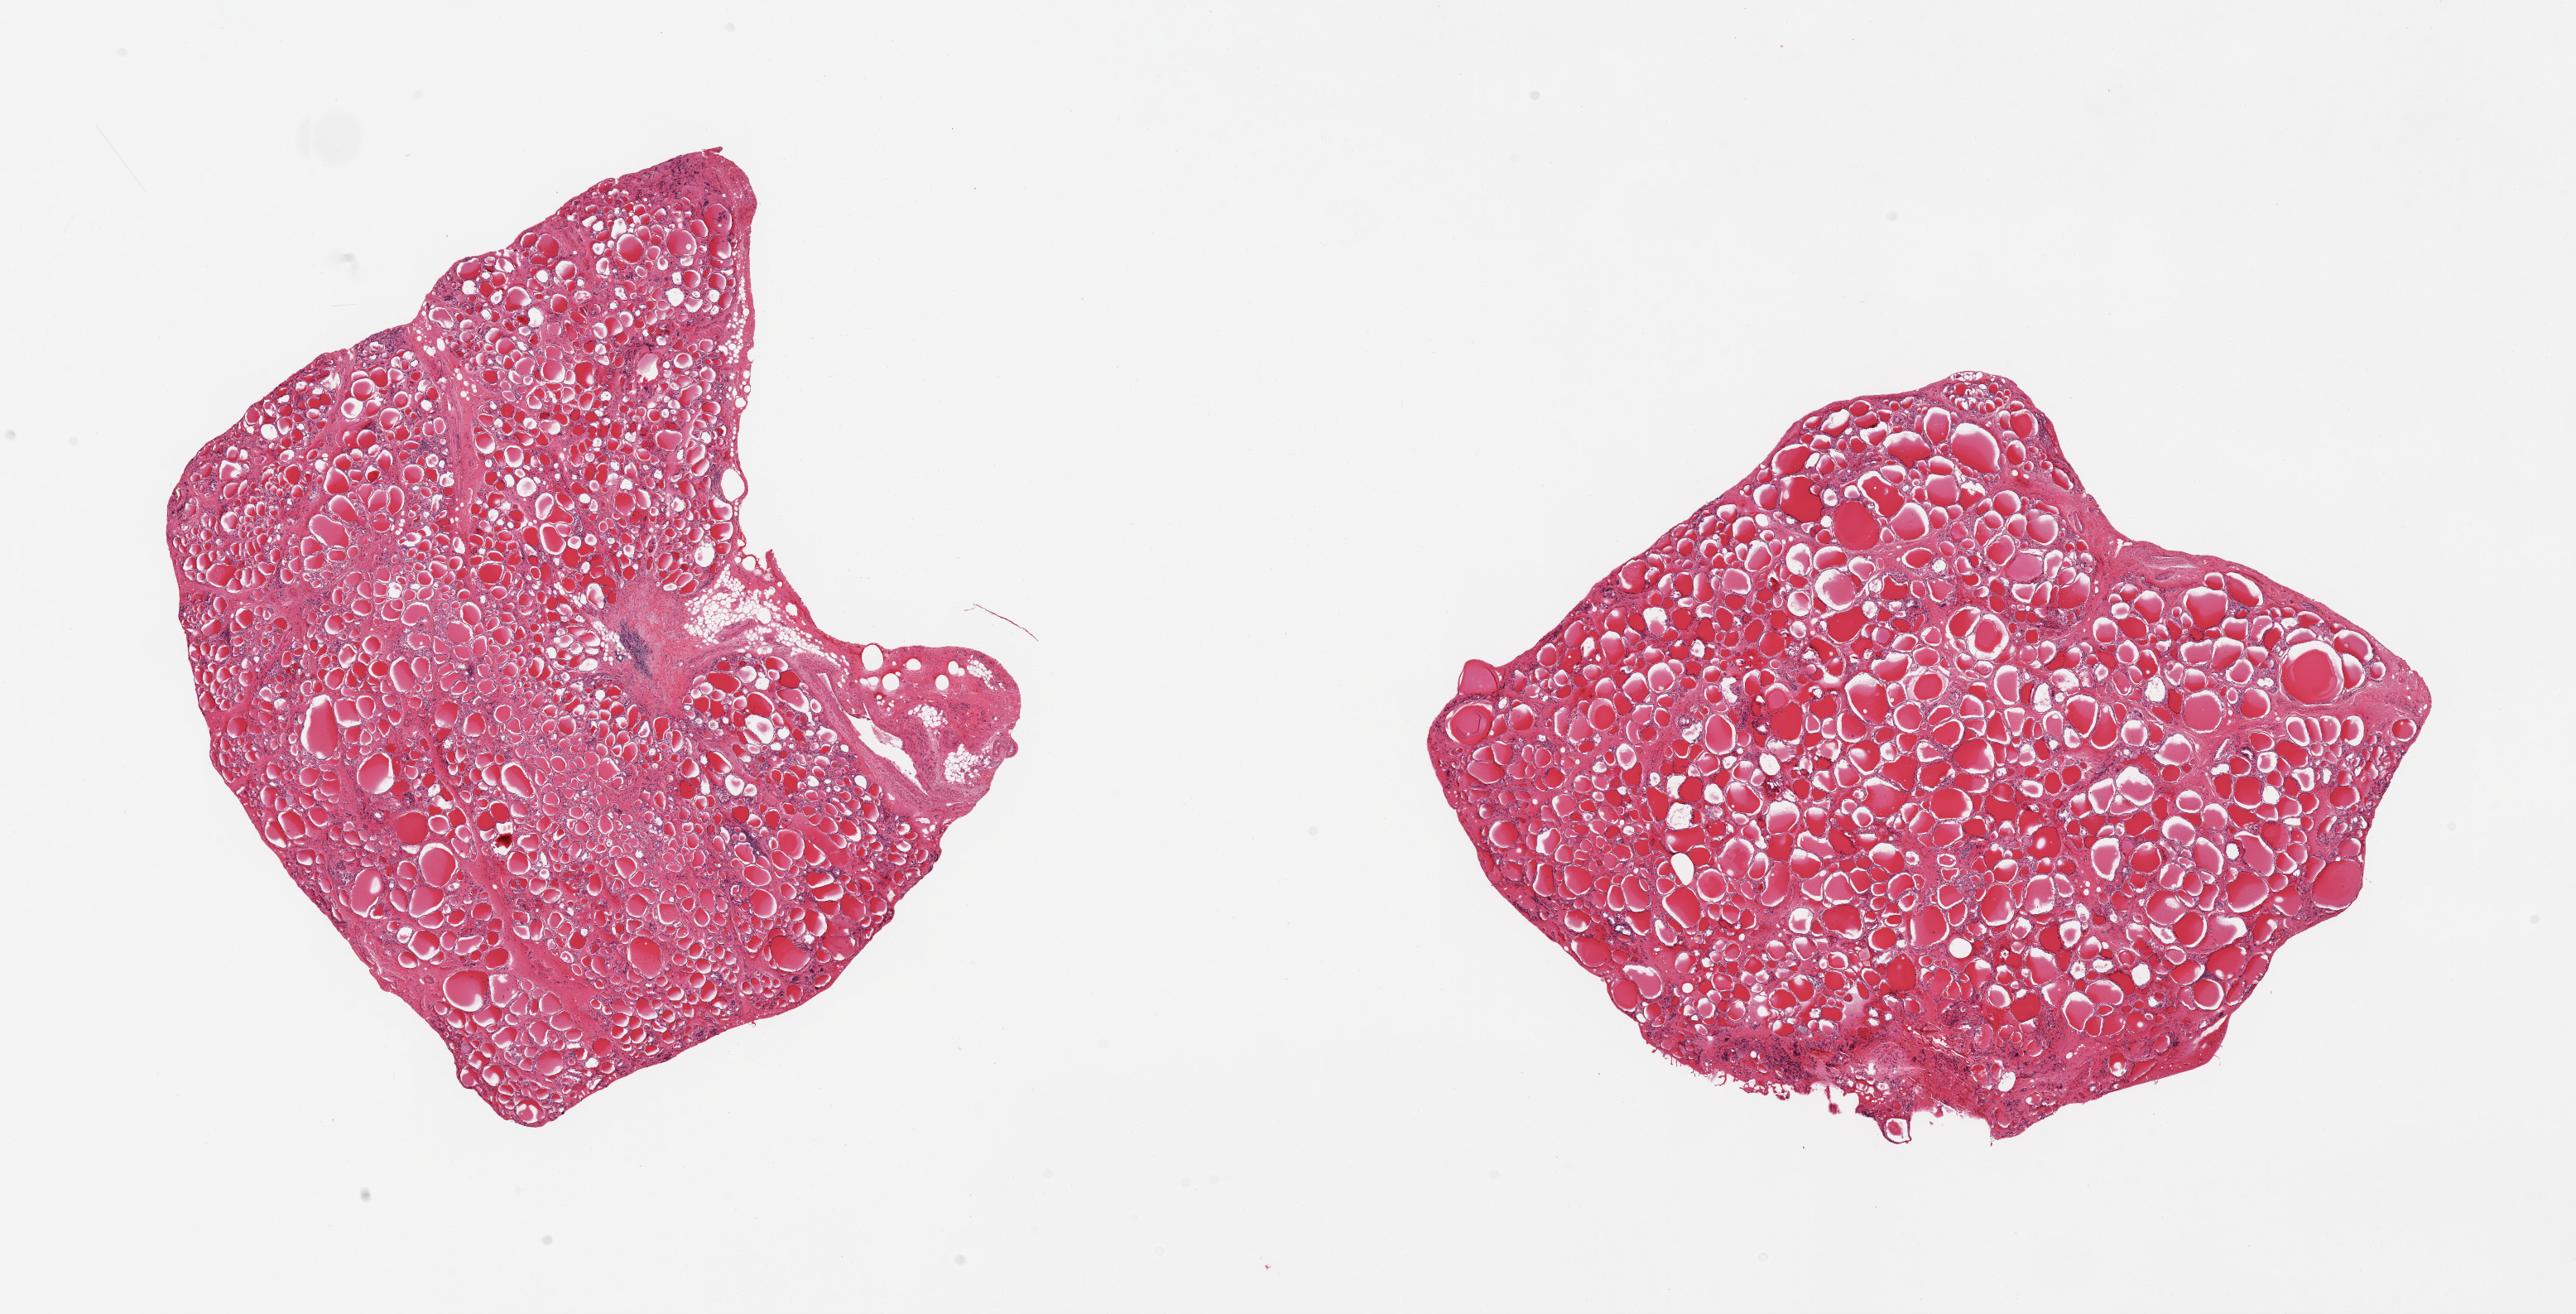
Whole-slide image, haematoxylin and eosin stain, brightfield — a low-resolution overview of the entire scanned area, about 24.6 x 12.6 mm (from a 20x scan), PAXgene-fixed, paraffin-embedded tissue, section of thyroid (target tissue), tissue donor sample.
• review note (as recorded): 2 pieces, no significant abnormalities, nubbin of fibrous tissue